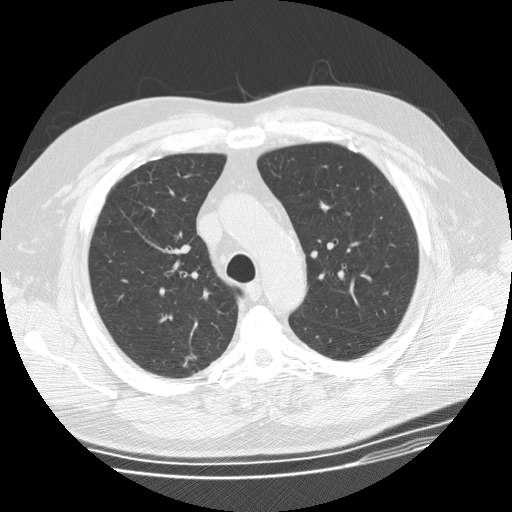
Low-dose screening chest CT, one axial slice; position 111 of 155 along the scan axis; reconstruction kernel STANDARD; 120 kVp; lung window (W 1500 / L -600 HU); 512 × 512 image matrix.
Structures marked on this image (expert manual segmentation):
- lesion 1 (tumor, upper lobe of right lung): box from (x=183, y=352) to (x=197, y=367) px